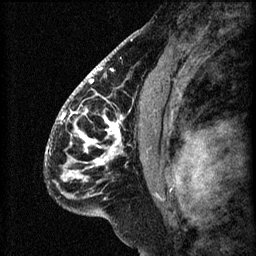
Breast MRI (dynamic contrast-enhanced), one sagittal slice; position 37 of 60 along the scan axis; 3 images stored at this slice position (order not interpretable as contrast timing); 1.5 T; TE 4.2 ms, TR 8.2 ms; 2.2 mm slice thickness; 256 × 256 image matrix, field of view 180 × 180 mm. Female patient, age 41 years.
Annotated regions visible in this slice (semi-automatically segmented with operator editing):
- analysis volume of interest (the breast-tissue region the enhancement analysis was run in; not a lesion): box from (x=56, y=104) to (x=157, y=201) px
- tumour enhancement mask (voxels above the 70 % enhancement threshold inside the analysis volume of interest): (x=63, y=110)–(x=123, y=183)